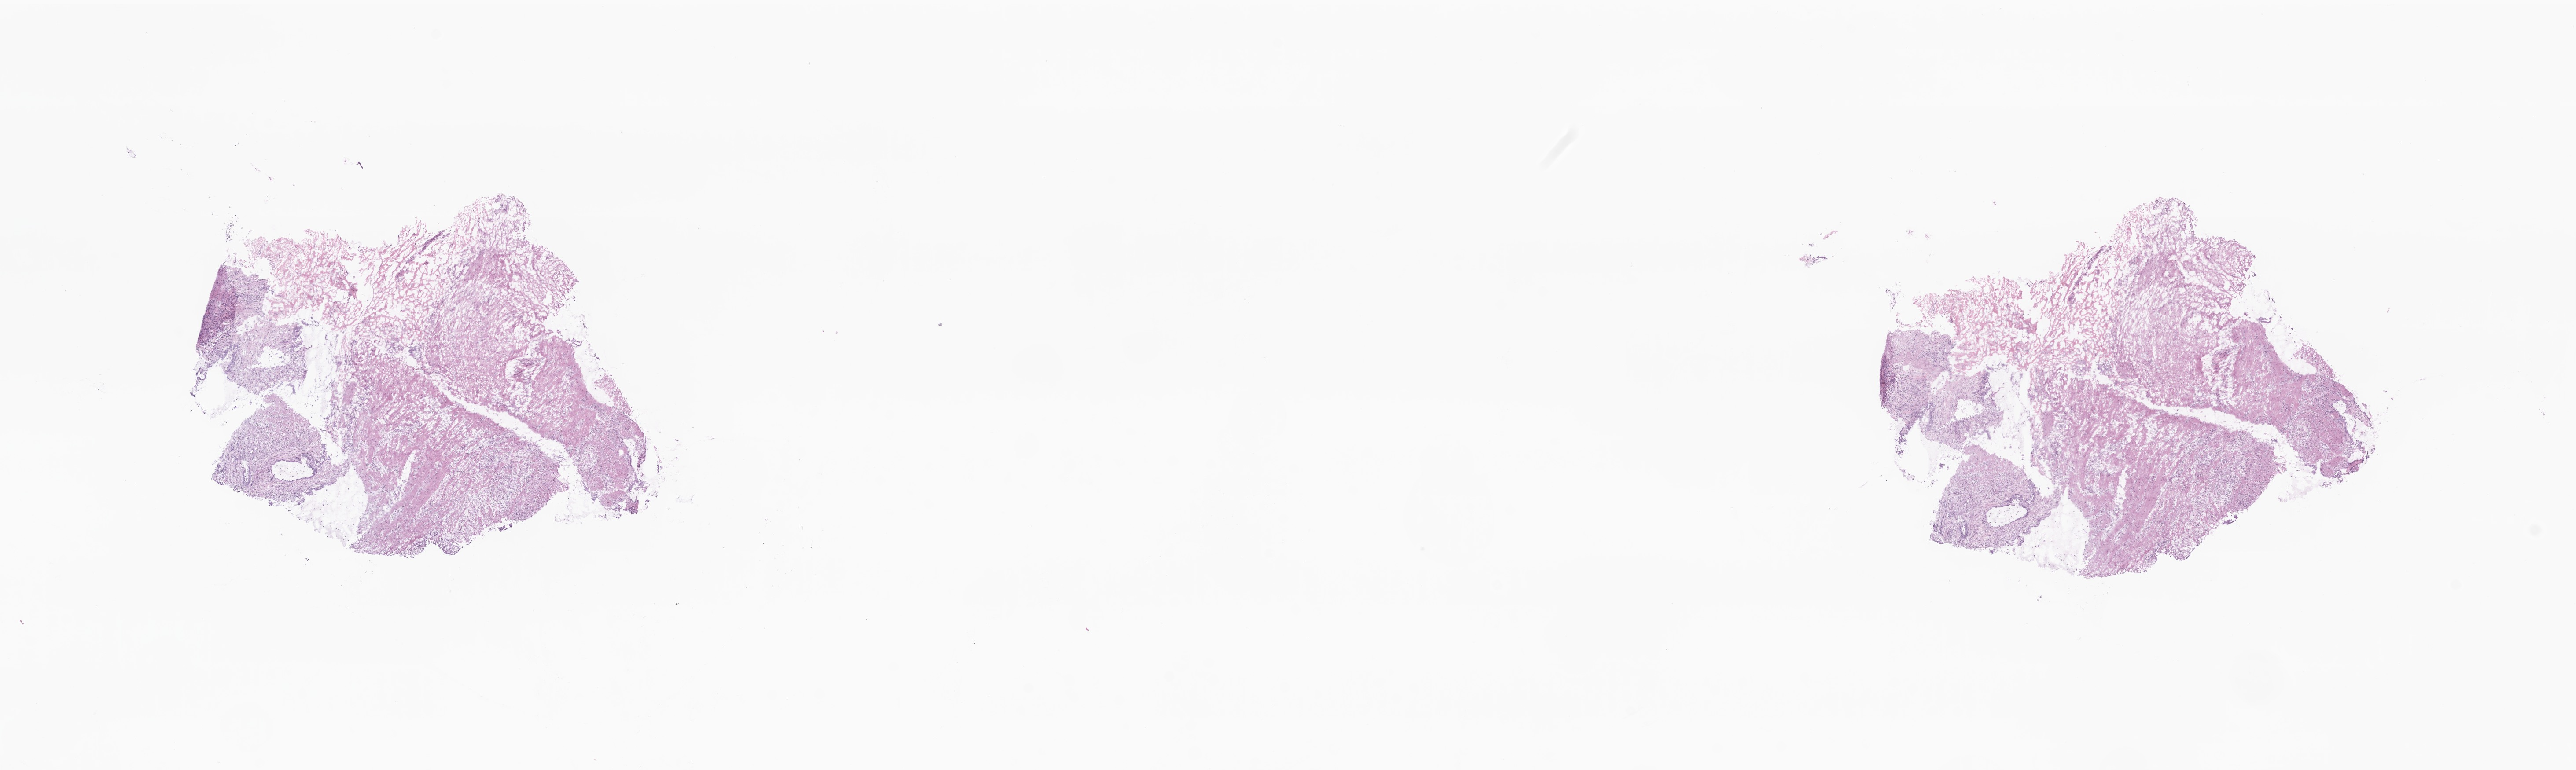
Whole-slide image, haematoxylin and eosin stain, shown as a low-resolution overview of the whole scanned area (about 24.7 x 7.4 mm); frozen section (tissue freezing medium); primary tumor; site: ascending colon. Male patient; age at initial diagnosis 62 years. Composition of this section per pathologist review: tumor cells 30%, tumor nuclei 30%, stromal cells 70%, necrosis 0%, normal cells 0%. Infiltration values recorded for this section: lymphocyte infiltration 3%, monocyte infiltration 2%, neutrophil infiltration 5%.
• diagnosis: Mucinous adenocarcinoma